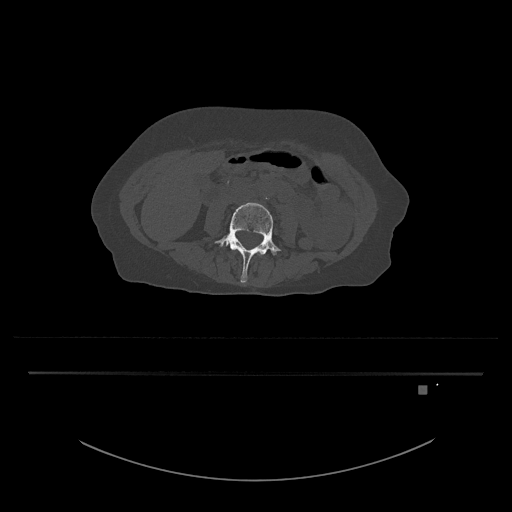
CT including the spine, one axial slice; slice 365 of 797 in the series (ordered by position); 120 kVp; bone window (W 1800 / L 400 HU); 0.5 mm slice thickness; 512 × 512 image matrix. Patient: female, 57 years. From the clinical record (not read from this slice): primary cancer: cervical.
Structures marked on this image (semi-automatic segmentation, software-assisted and operator-edited):
- L3 vertebra: bounding box (x1, y1, x2, y2) in pixels: (259, 254, 261, 256)
- L4 vertebra: (213, 202, 282, 283)